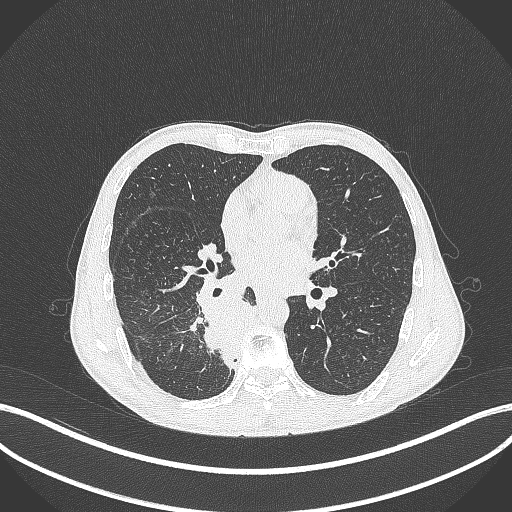
Chest CT, one axial slice; slice 186 of 371 in the series (ordered by position); 120 kVp; lung window (W 1500 / L -600 HU); 1 mm slice thickness; 512 × 512 image matrix, field of view 400 × 400 mm. Male patient, age 58 years. From the clinical record (not read from this slice): clinical TNM (as recorded): T3 N1 M1.
Structures marked on this image (bounding box drawn by a radiologist):
- lung tumour (recorded histology: squamous cell carcinoma): bounding box [x1, y1, x2, y2] px = [188, 289, 267, 367]